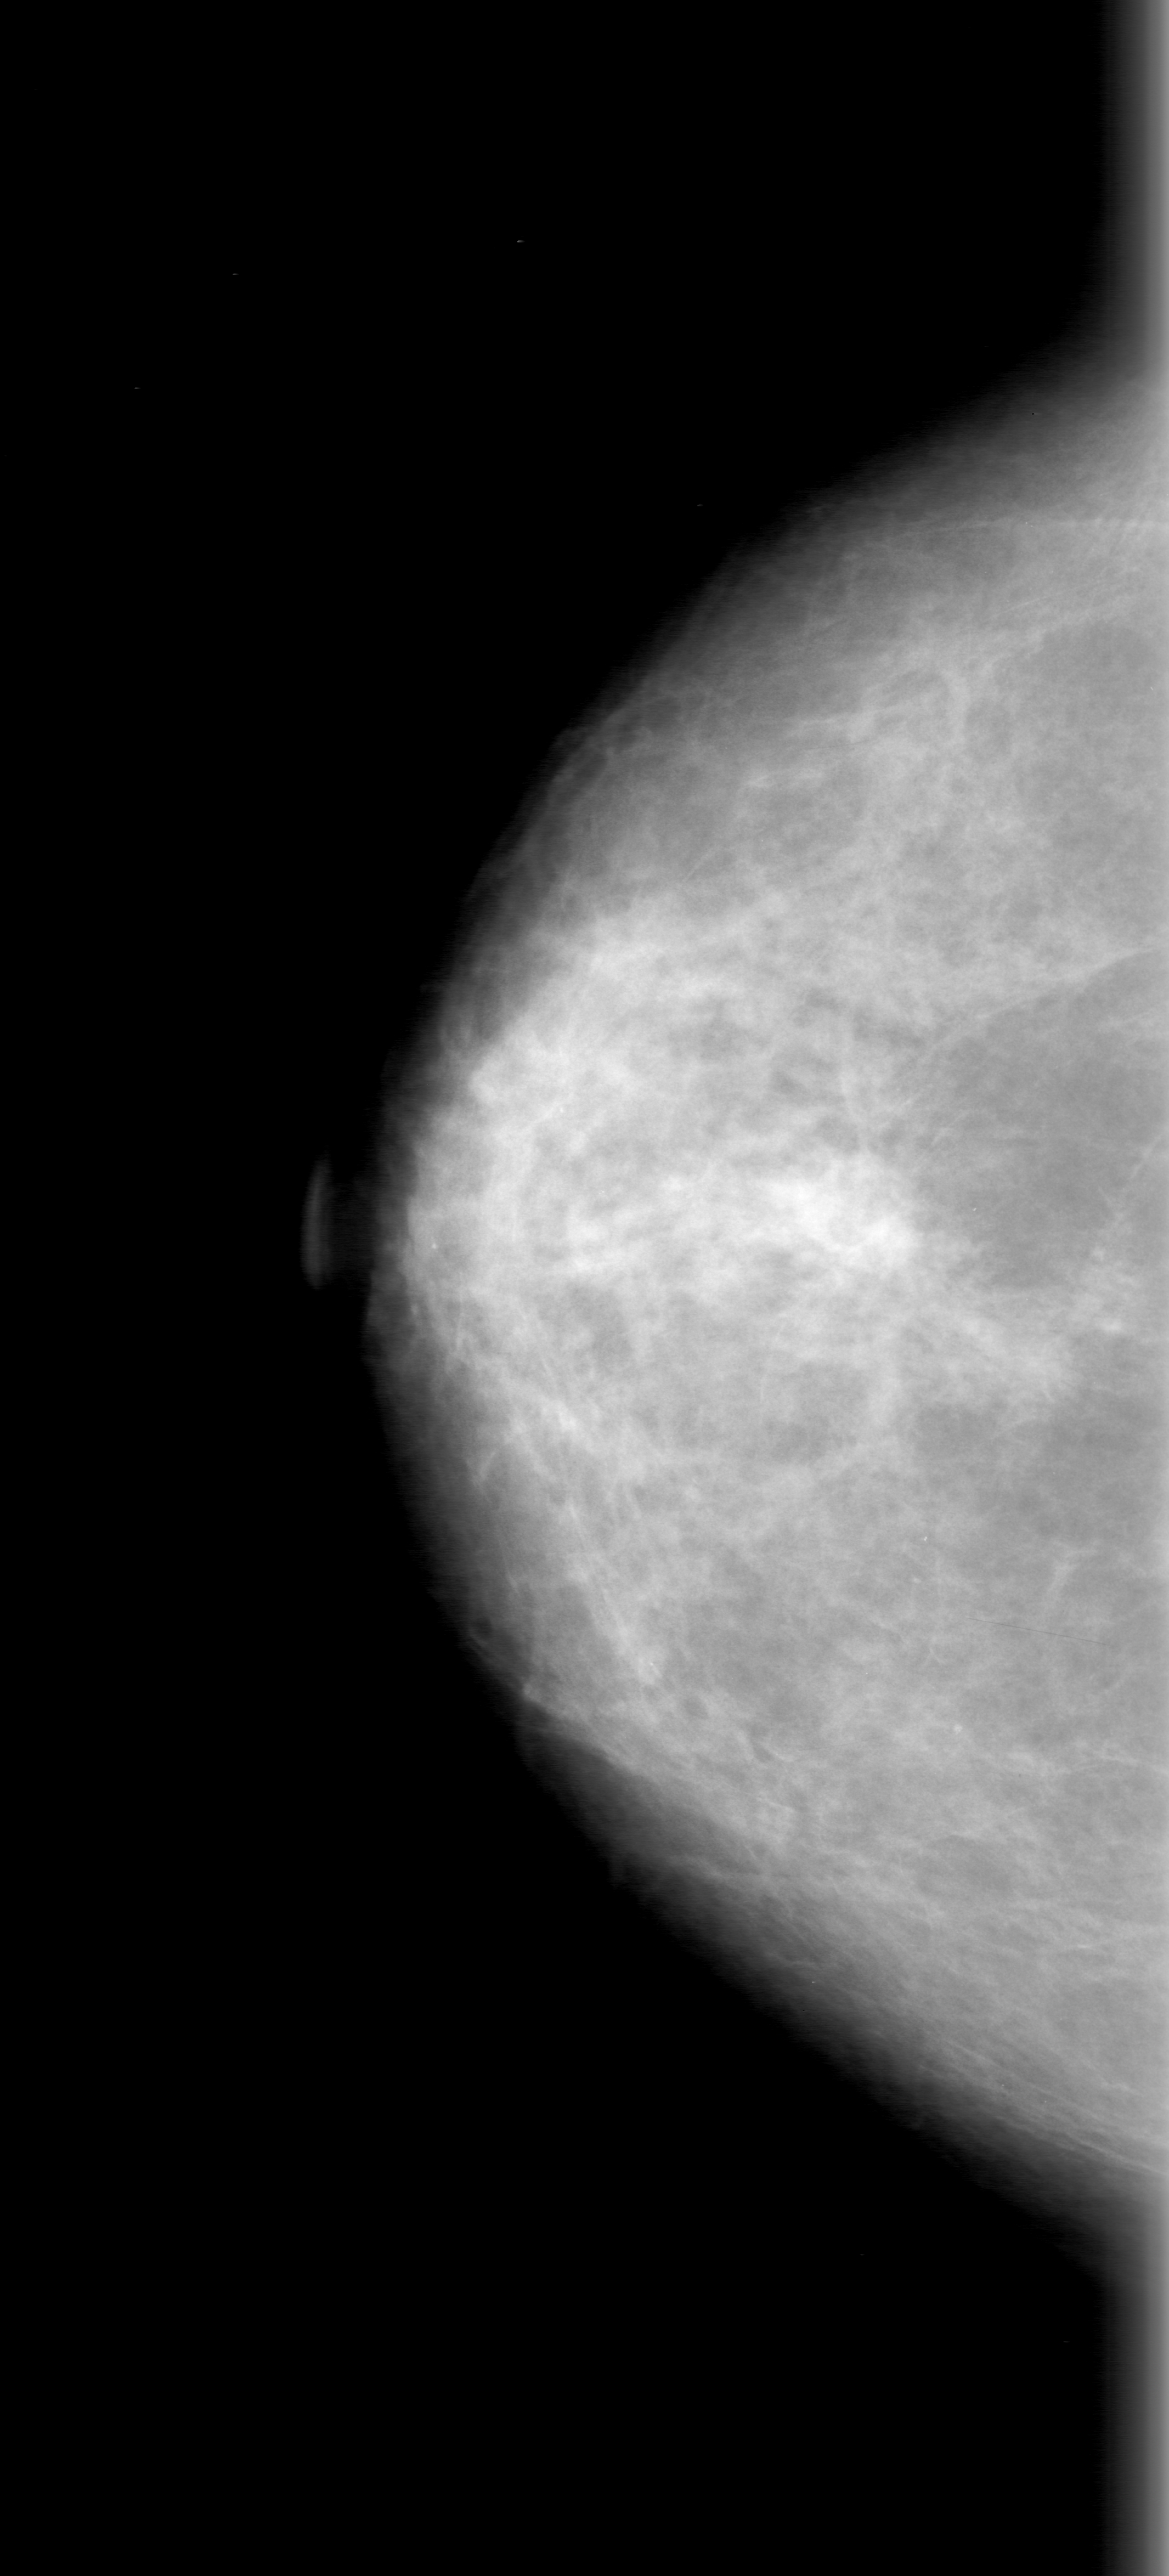
Mammogram (digitized film), right breast, CC view, BI-RADS breast density category 2 (scale 1–4).
- Abnormality record for this image: mass, shape oval, margins obscured; BI-RADS assessment category 0 (incomplete: needs additional imaging); pathology result (as recorded, not read from the image): malignant.